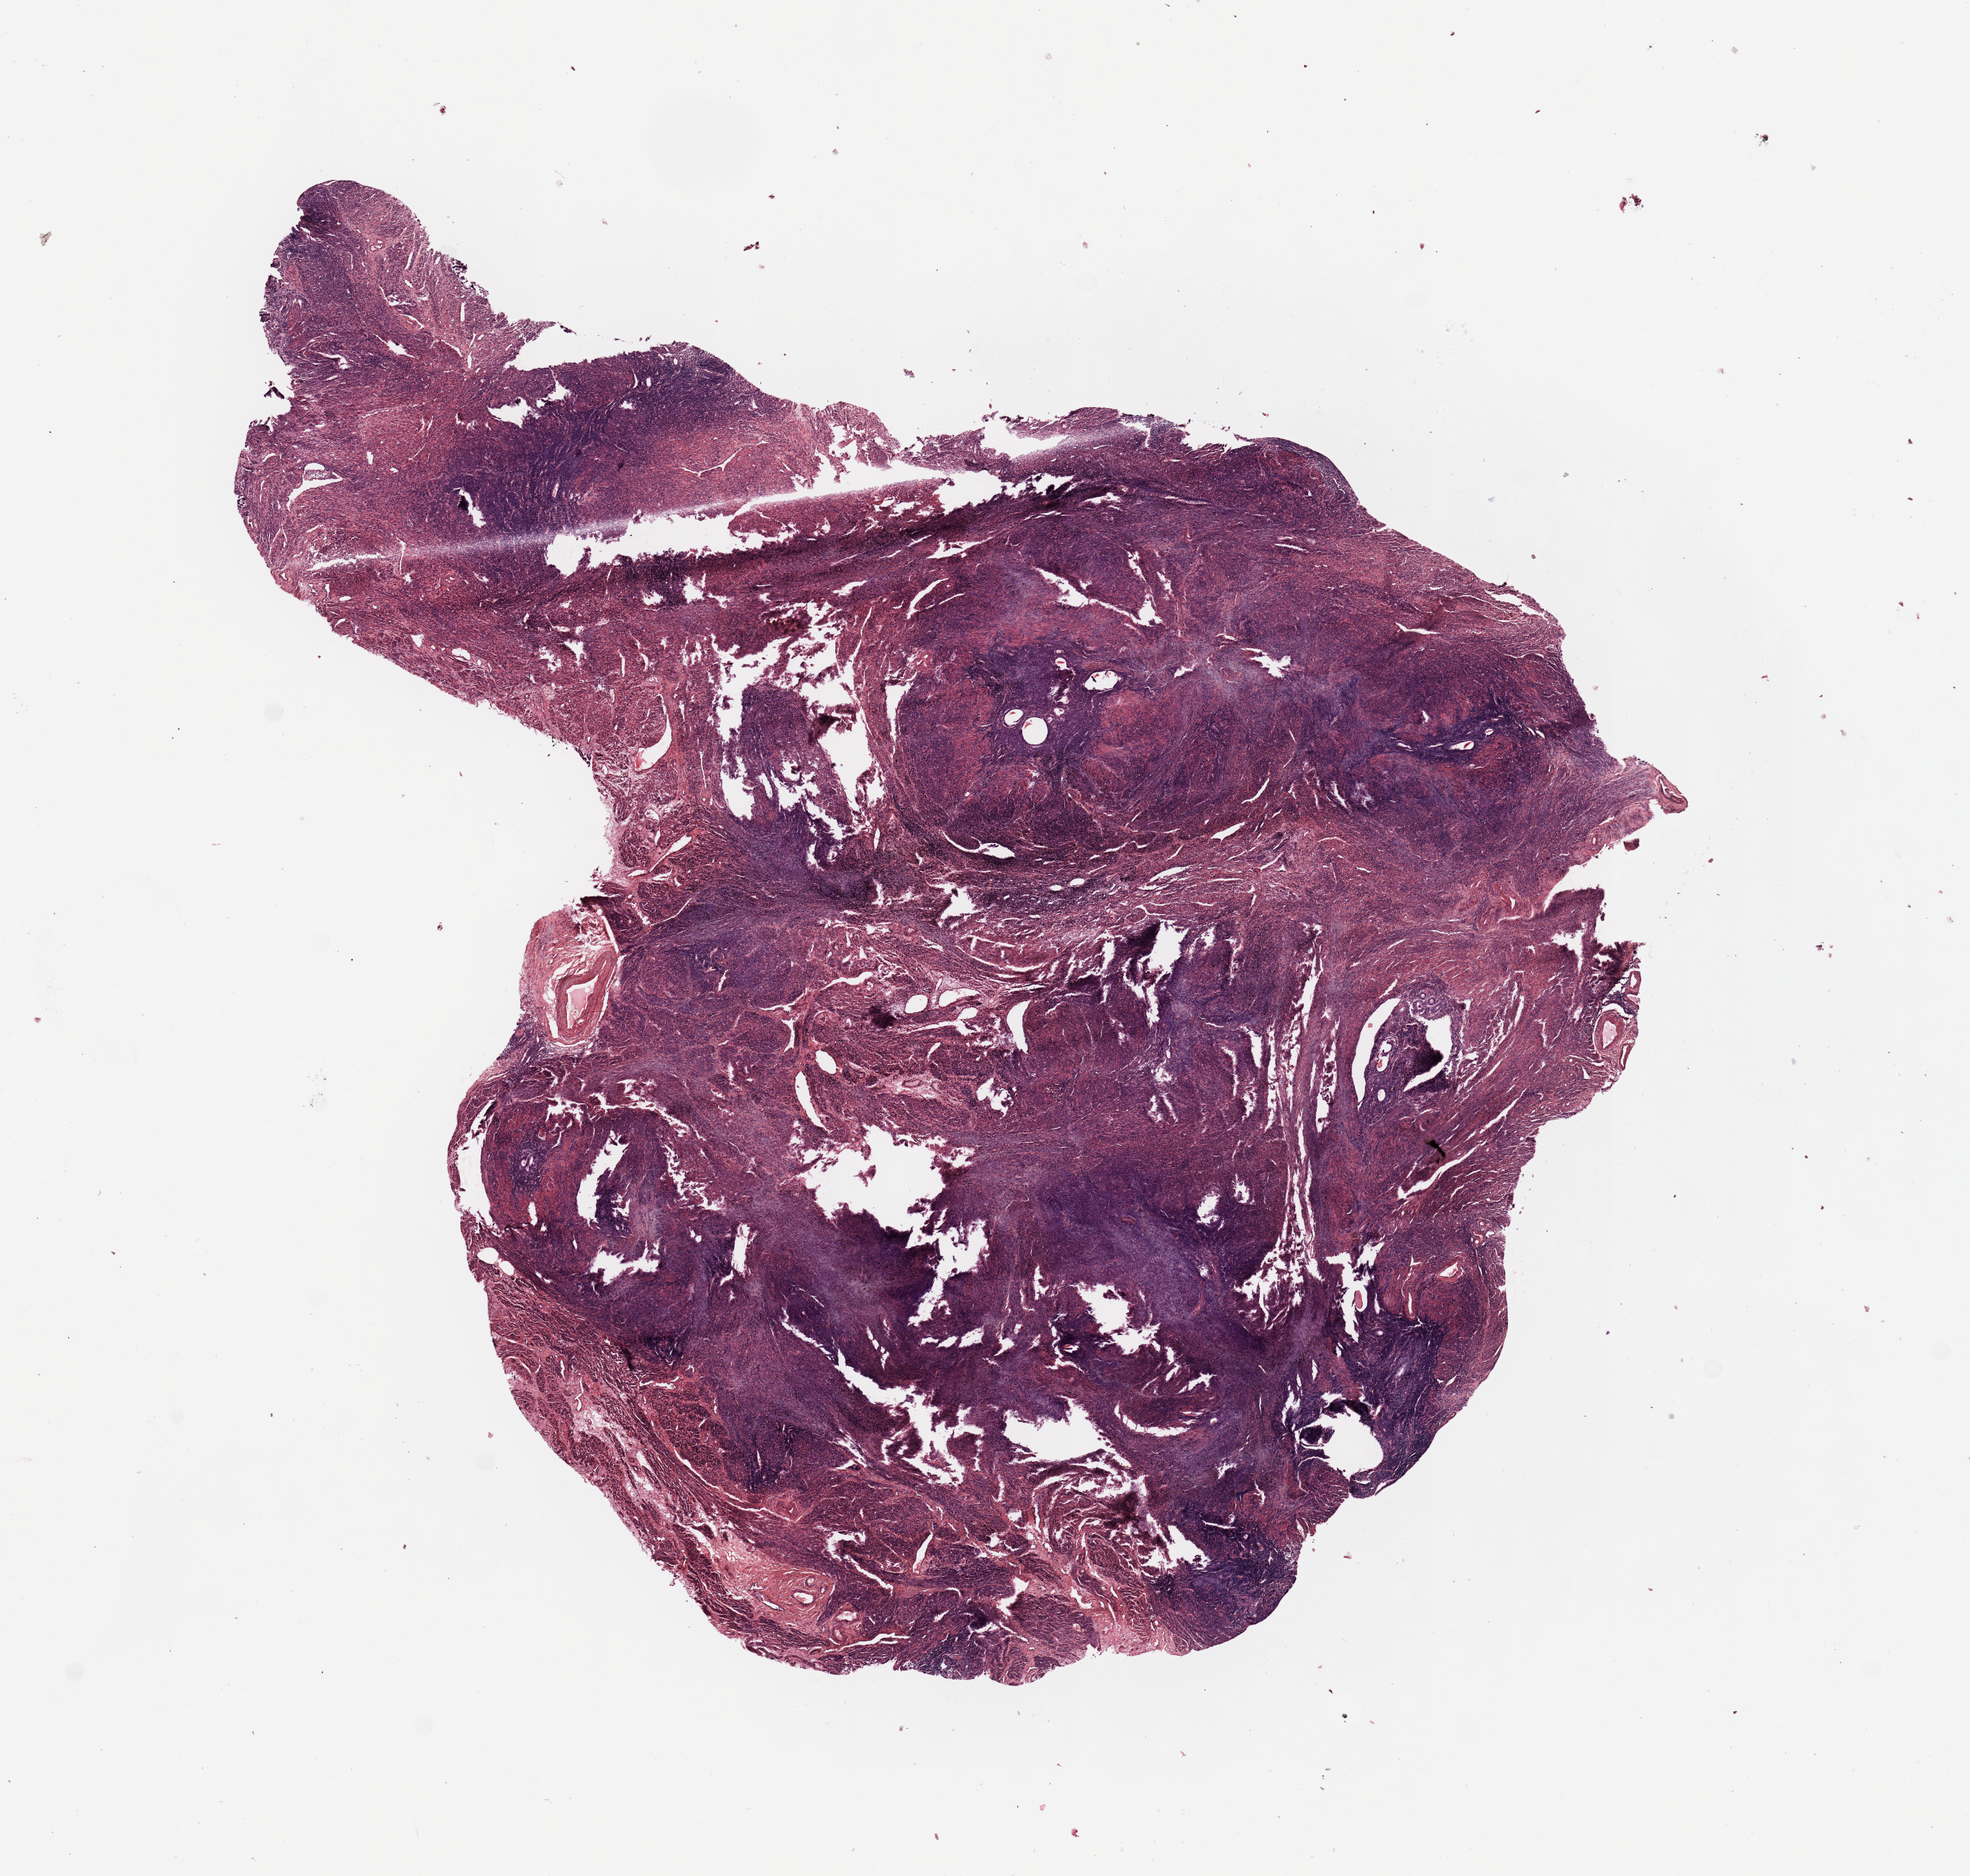
H&E-stained whole-slide image, low-resolution overview of the scanned area, about 10.8 x 10.3 mm (acquisition: 20x scan), normal (non-tumour) tissue sample, sampled site: uterus. Female, 68 y/o.
• this section: normal (non-tumour) tissue from the same patient
• patient diagnosis: Endometrioid adenocarcinoma, NOS